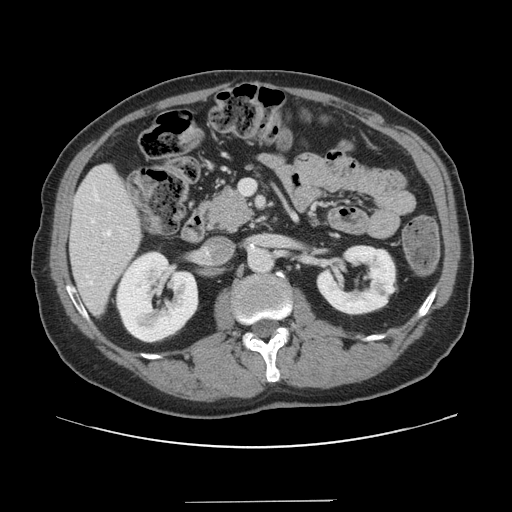
Contrast-enhanced abdominal CT, one axial slice; slice 63 of 151 in the series (ordered by position); soft-tissue window (W 400 / L 40 HU); 2.5 mm slice thickness; 512 × 512 image matrix. Male patient, age 63 years. From the clinical record (not read from this slice): diagnosis: colorectal cancer liver metastases, imaged before liver resection; multiple liver metastases: no; largest metastasis: 2.1 cm.
Outlined on this slice (expert manual segmentation):
- hepatic veins: bounding box [x1, y1, x2, y2] px = [89, 230, 111, 284]
- liver: [72, 166, 141, 315]
- planned liver remnant (the part of the liver to remain after resection): [71, 166, 141, 315]
- portal vein (with intrahepatic branches): [240, 180, 255, 195]